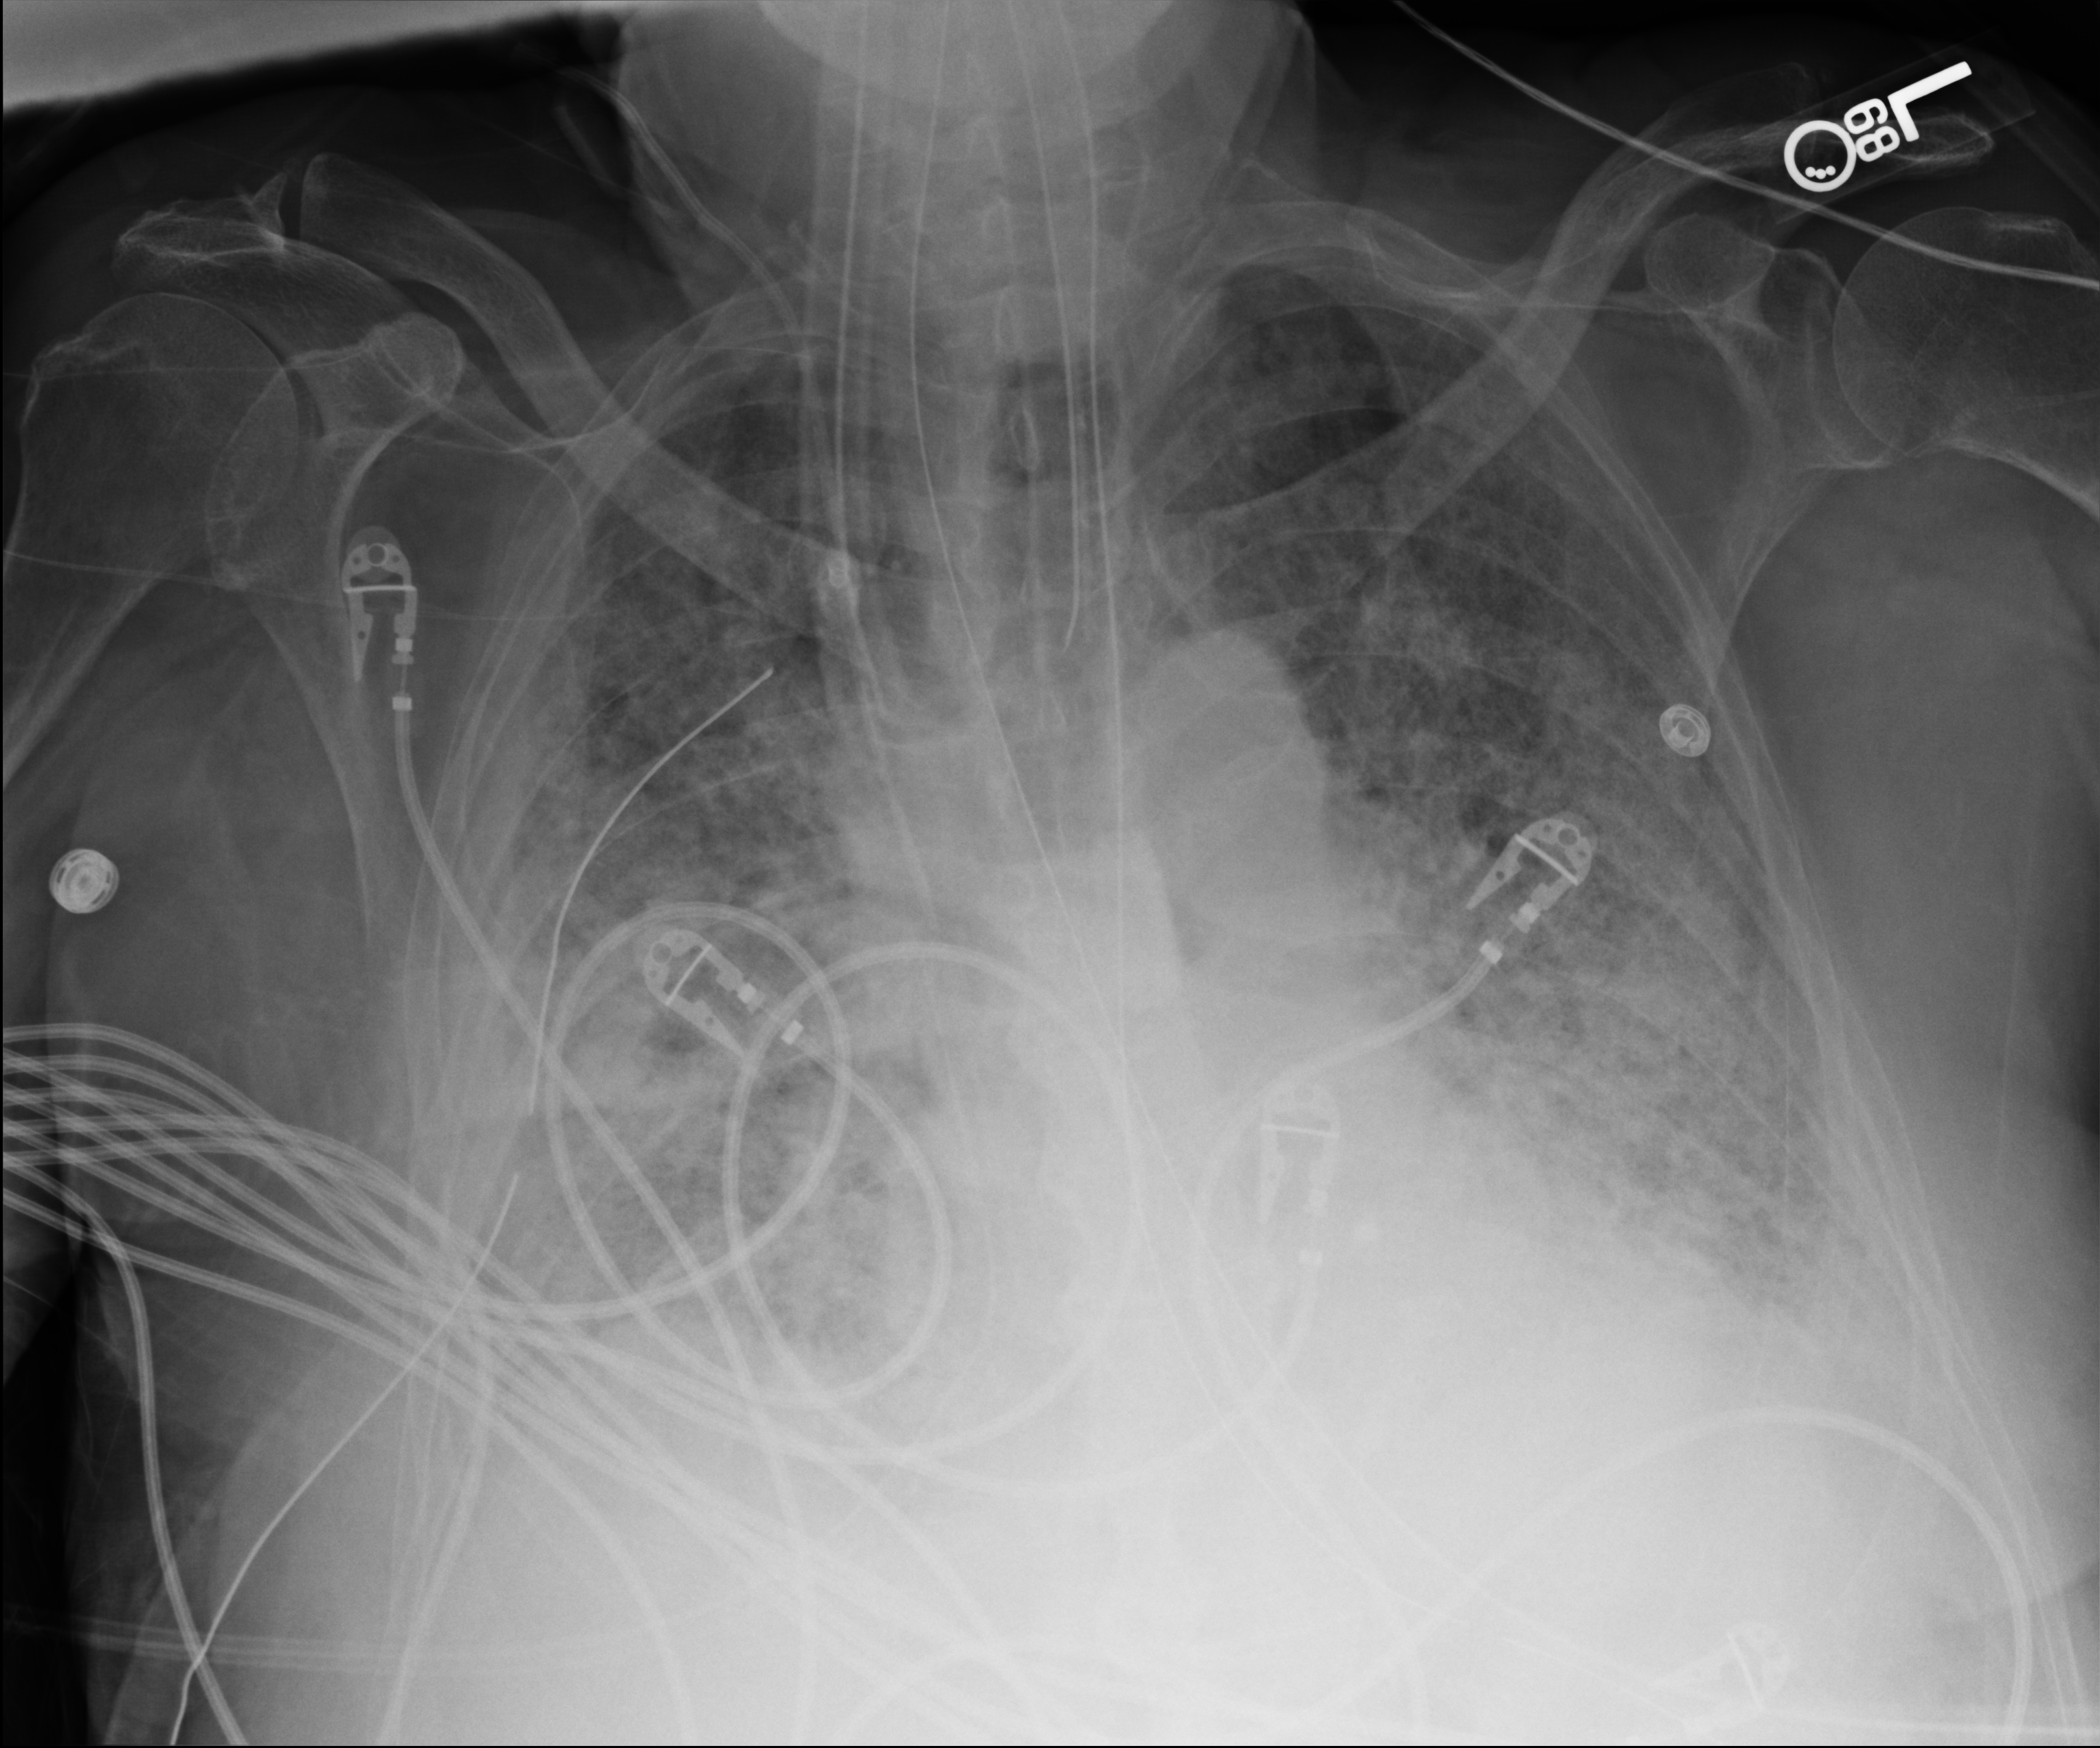
Bedside chest radiograph (computed radiography), anteroposterior (AP) projection. Male patient hospitalised with COVID-19, age 75–90 years.
Hospital-stay facts (about this admission, not read from this image; timing relative to this image not recorded): other chronic lung disease (admission record): no; admitted to intensive care during this hospital stay: yes.